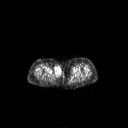
FDG PET of an extremity soft-tissue mass (from a PET/CT study), one axial slice. Slice 233 of 311 in the series (ordered by position). 3.27 mm slice thickness. 128 × 128 image matrix. Female patient, age 78 years. From the clinical record (not read from this slice): histological type: leiomyosarcoma; grade: intermediate; site of the primary tumour: parascapusular.
Outlined on this slice (expert contour drawn on MRI and transferred to this co-registered scan by the dataset authors):
- gross tumour volume including surrounding oedema: bounding box (x1, y1, x2, y2) in pixels: (53, 65, 62, 76)
- gross tumour volume (mass): (53, 65, 62, 76)